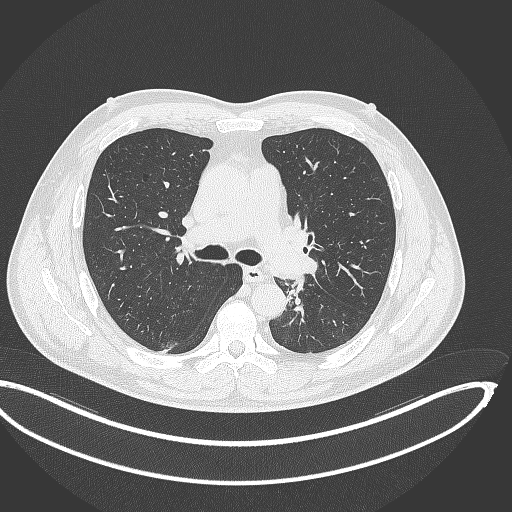
Chest CT, one axial slice; position 222 of 362 along the scan axis; lung window (W 1500 / L -600 HU); 512 × 512 image matrix, field of view 442 × 442 mm. Patient: male, 50 years. From the clinical record (not read from this slice): clinical TNM (as recorded): T2a N3 M0.
Annotated regions visible in this slice (rectangle marked by the reading radiologist):
- lung tumour (recorded histology: squamous cell carcinoma): box from (x=286, y=272) to (x=309, y=322) px